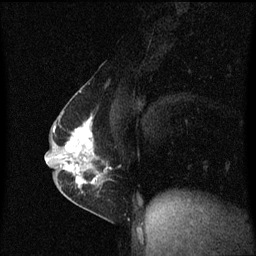
Breast MRI (dynamic contrast-enhanced), one sagittal slice; position 31 of 60 along the scan axis; dynamic contrast-enhanced series, image 2 of 3 at this slice position (ordered by acquisition); 1.5 T; TE 4.2 ms, TR 8.4 ms; 2 mm slice thickness; 256 × 256 image matrix, field of view 200 × 200 mm. Female patient, age 40 years.
Annotated regions visible in this slice (semi-automatic segmentation, software-assisted and operator-edited):
- analysis volume of interest (the breast-tissue region the enhancement analysis was run in; not a lesion): bounding box <57,110,111,191> (left, top, right, bottom; pixels)
- tumour enhancement mask (voxels above the 70 % enhancement threshold inside the analysis volume of interest): <64,116,107,189>